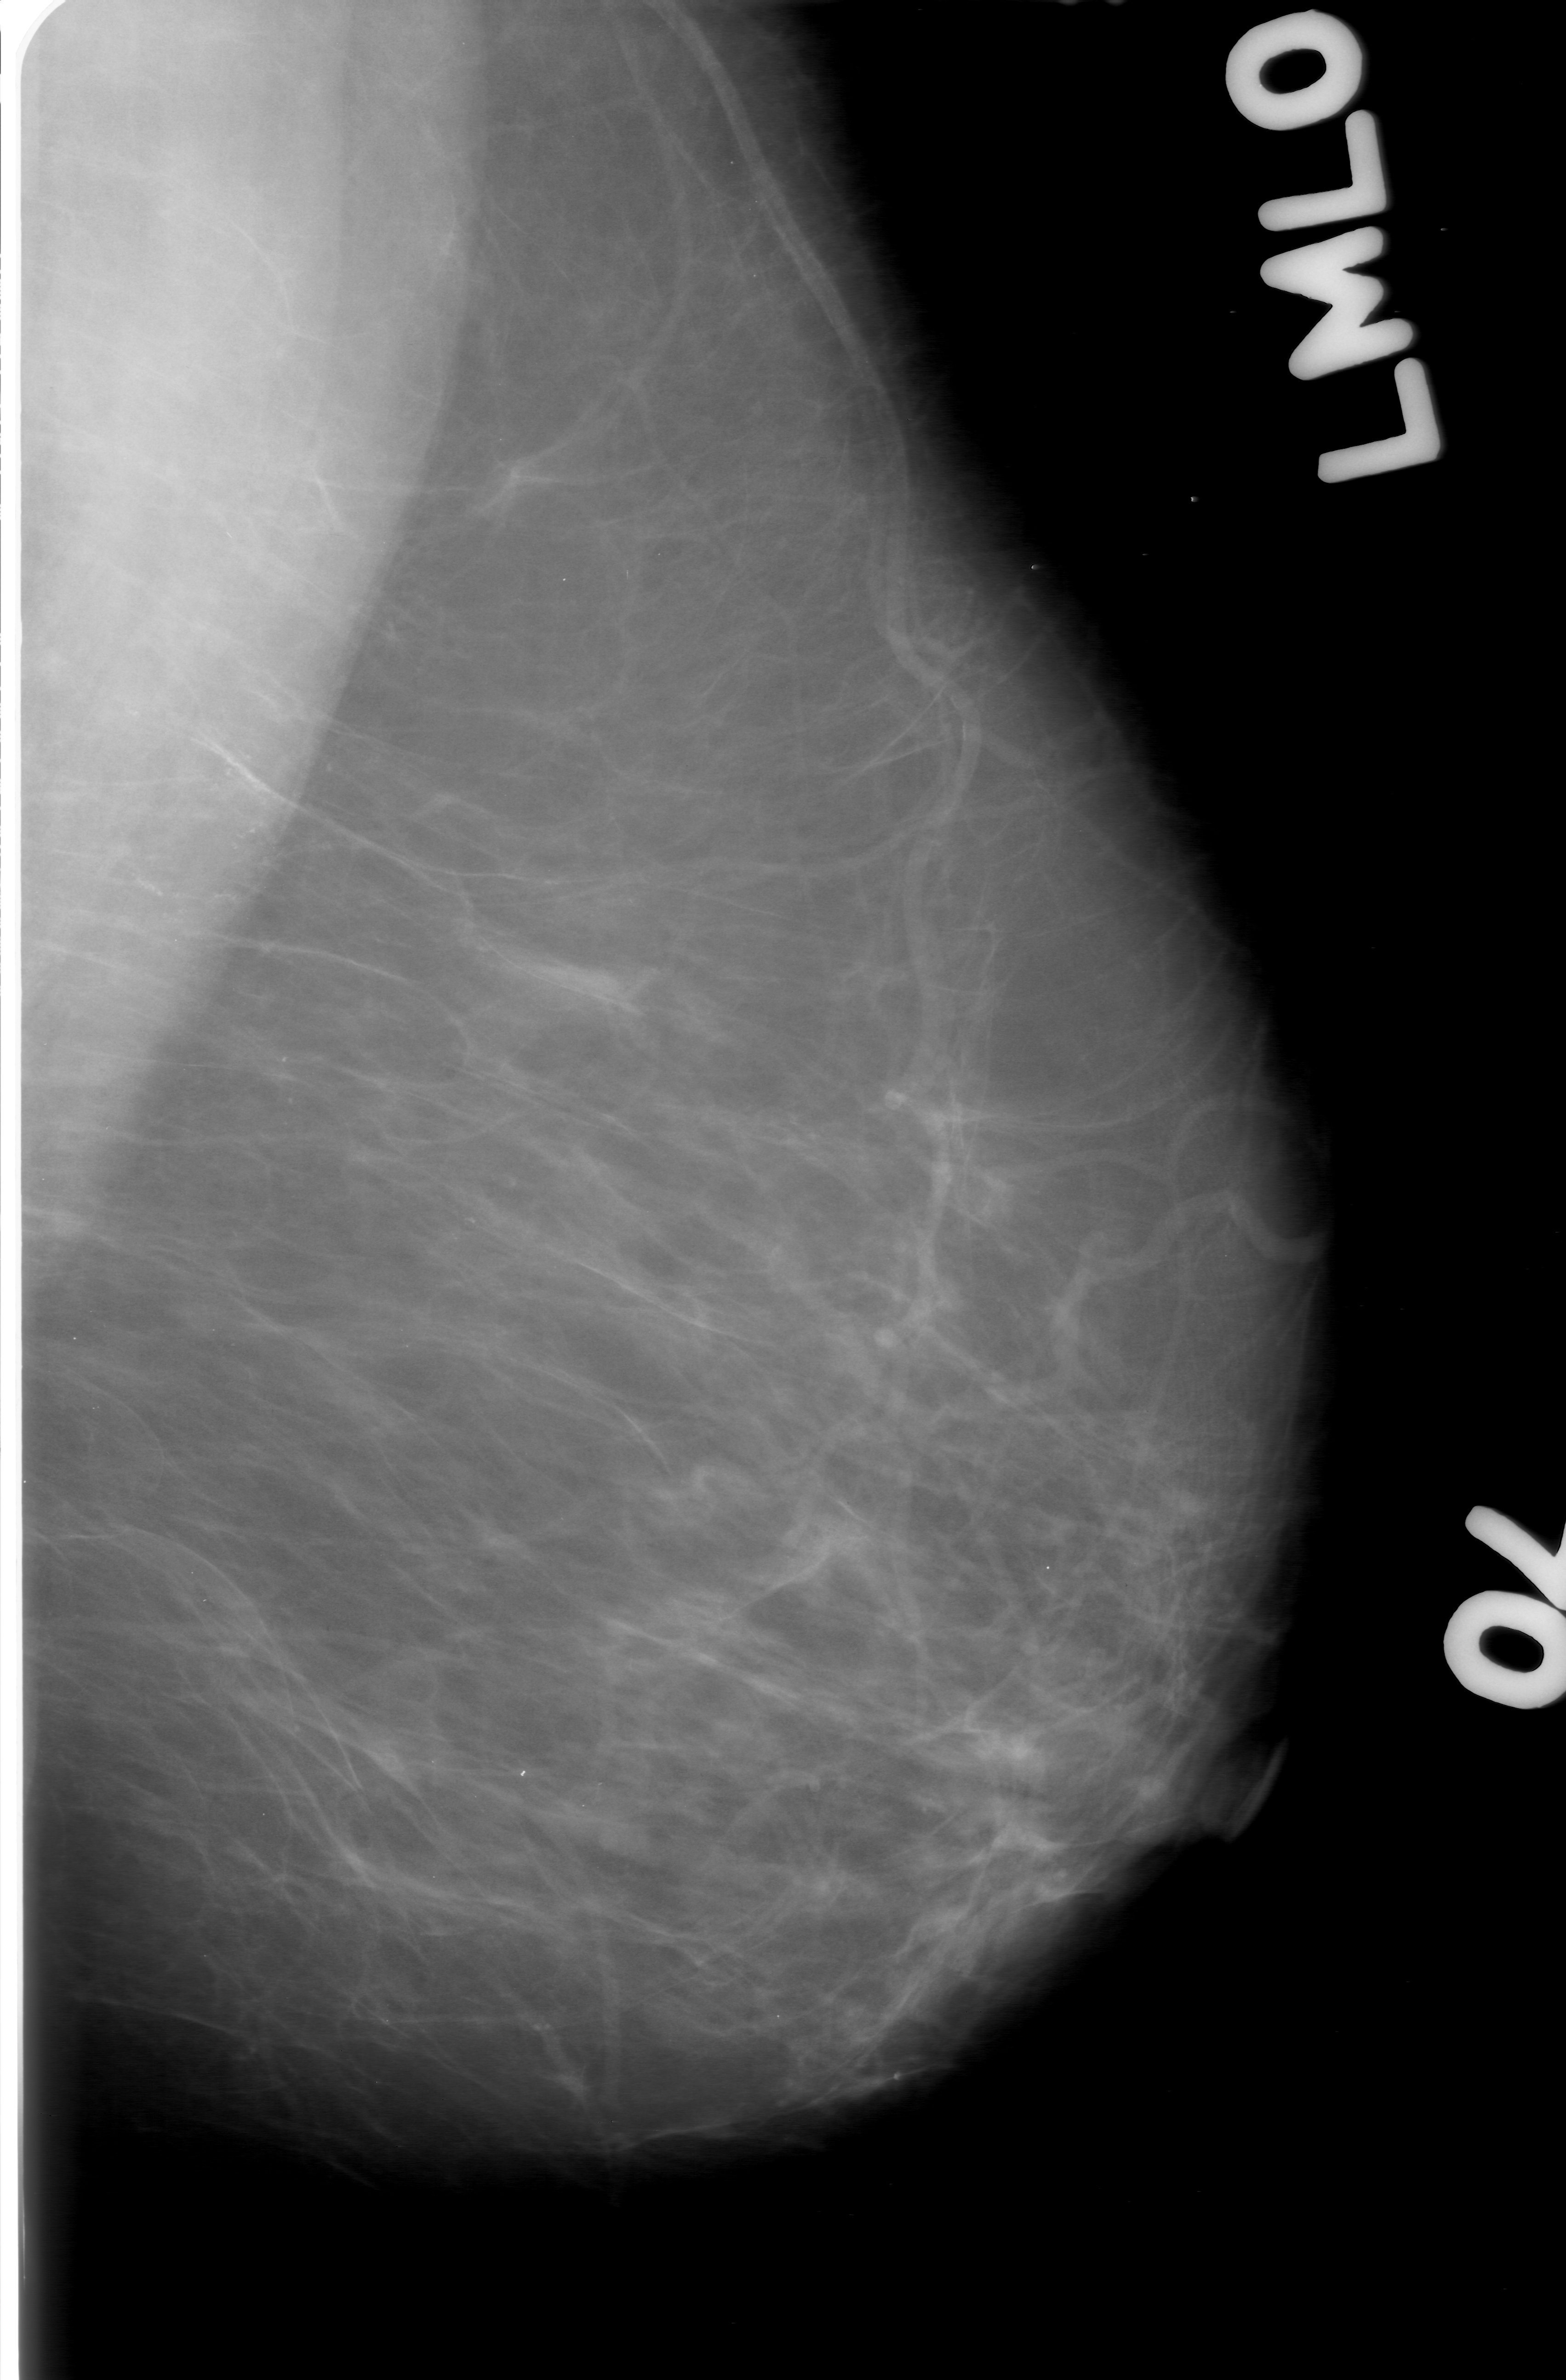
Digitized screen-film mammogram. Left breast. MLO view. BI-RADS breast density category 2 (scale 1–4). 1566 × 2380 image matrix.
Expert-marked regions of interest on this image (one box per marked abnormality):
- calcifications, morphology amorphous, distribution linear; BI-RADS assessment category 3; pathology (as recorded): malignant: bounding box (x1, y1, x2, y2) in pixels: (57, 618, 515, 1019)